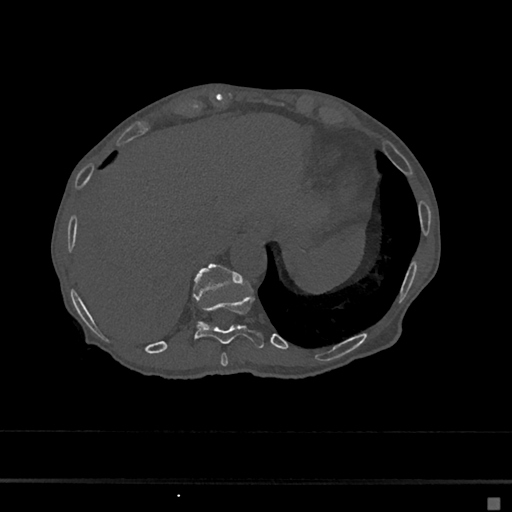
CT including the spine, one axial slice; position 216 of 797 along the scan axis; reconstruction kernel Br40s/3; 120 kVp; bone window (W 1800 / L 400 HU); 512 × 512 image matrix, field of view 360 × 360 mm. Patient: female, 68 years. Case-level facts recorded for this patient, not image findings: primary cancer: renal.
Annotated regions visible in this slice (semi-automatic segmentation, software-assisted and operator-edited):
- T10 vertebra: bounding box [x1, y1, x2, y2] px = [193, 293, 264, 348]
- T11 vertebra: [193, 263, 243, 324]
- T9 vertebra: [220, 352, 228, 367]